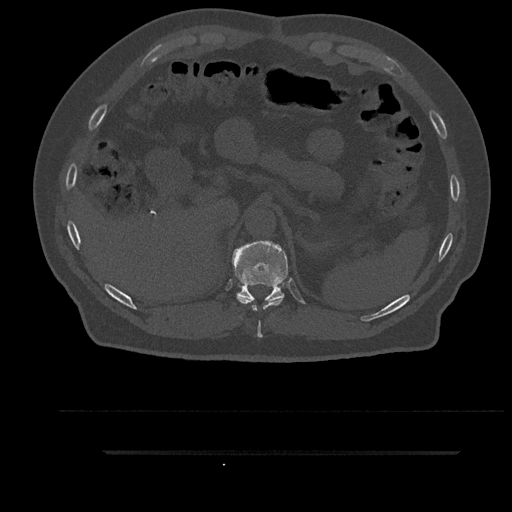
CT including the spine, one axial slice. Position 332 of 797 along the scan axis. Reconstruction kernel Br40s/3. 120 kVp. Bone window (W 1800 / L 400 HU). 0.5 mm slice thickness. 512 × 512 image matrix, field of view 432 × 432 mm. Patient: male, 63 years. From the clinical record (not read from this slice): primary cancer: renal; vertebrae with lytic lesions (as recorded): T8.
Annotated regions visible in this slice (semi-automatically segmented with operator editing):
- T10 vertebra: bounding box [x1, y1, x2, y2] px = [237, 297, 284, 338]
- T11 vertebra: [232, 241, 288, 302]